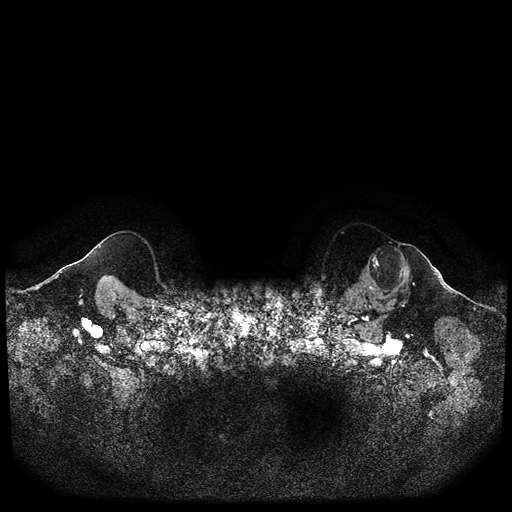
Breast MRI (dynamic contrast-enhanced, multi-phase), one axial slice; slice 98 of 116 in the series (ordered by position); dynamic contrast-enhanced series, time point 2 of 5 at this slice position (early post-contrast); 1.5 T; TE 2.6 ms, TR 5.3 ms; 2 mm slice thickness; 512 × 512 image matrix, field of view 350 × 350 mm. Female patient, age 64 years.
Structures marked on this image (semi-automatically segmented with operator editing):
- breast lesion (labelled 'tumour' in the annotation; benign lesions carry a separate 'benign' label): bounding box [x1, y1, x2, y2] px = [363, 242, 410, 302]